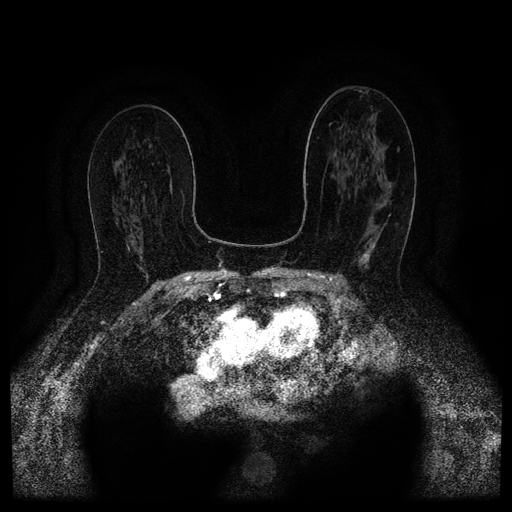
Breast MRI (dynamic contrast-enhanced, multi-phase), one axial slice; position 61 of 116 along the scan axis; dynamic contrast-enhanced series, time point 2 of 5 at this slice position (early post-contrast); 1.5 T; TE 2.6 ms, TR 5.4 ms; 512 × 512 image matrix. Patient: female, 67 years.
Annotated regions visible in this slice (semi-automatic segmentation, software-assisted and operator-edited):
- breast lesion (labelled 'tumour' in the annotation; benign lesions carry a separate 'benign' label): bounding box (x1, y1, x2, y2) in pixels: (359, 214, 391, 269)